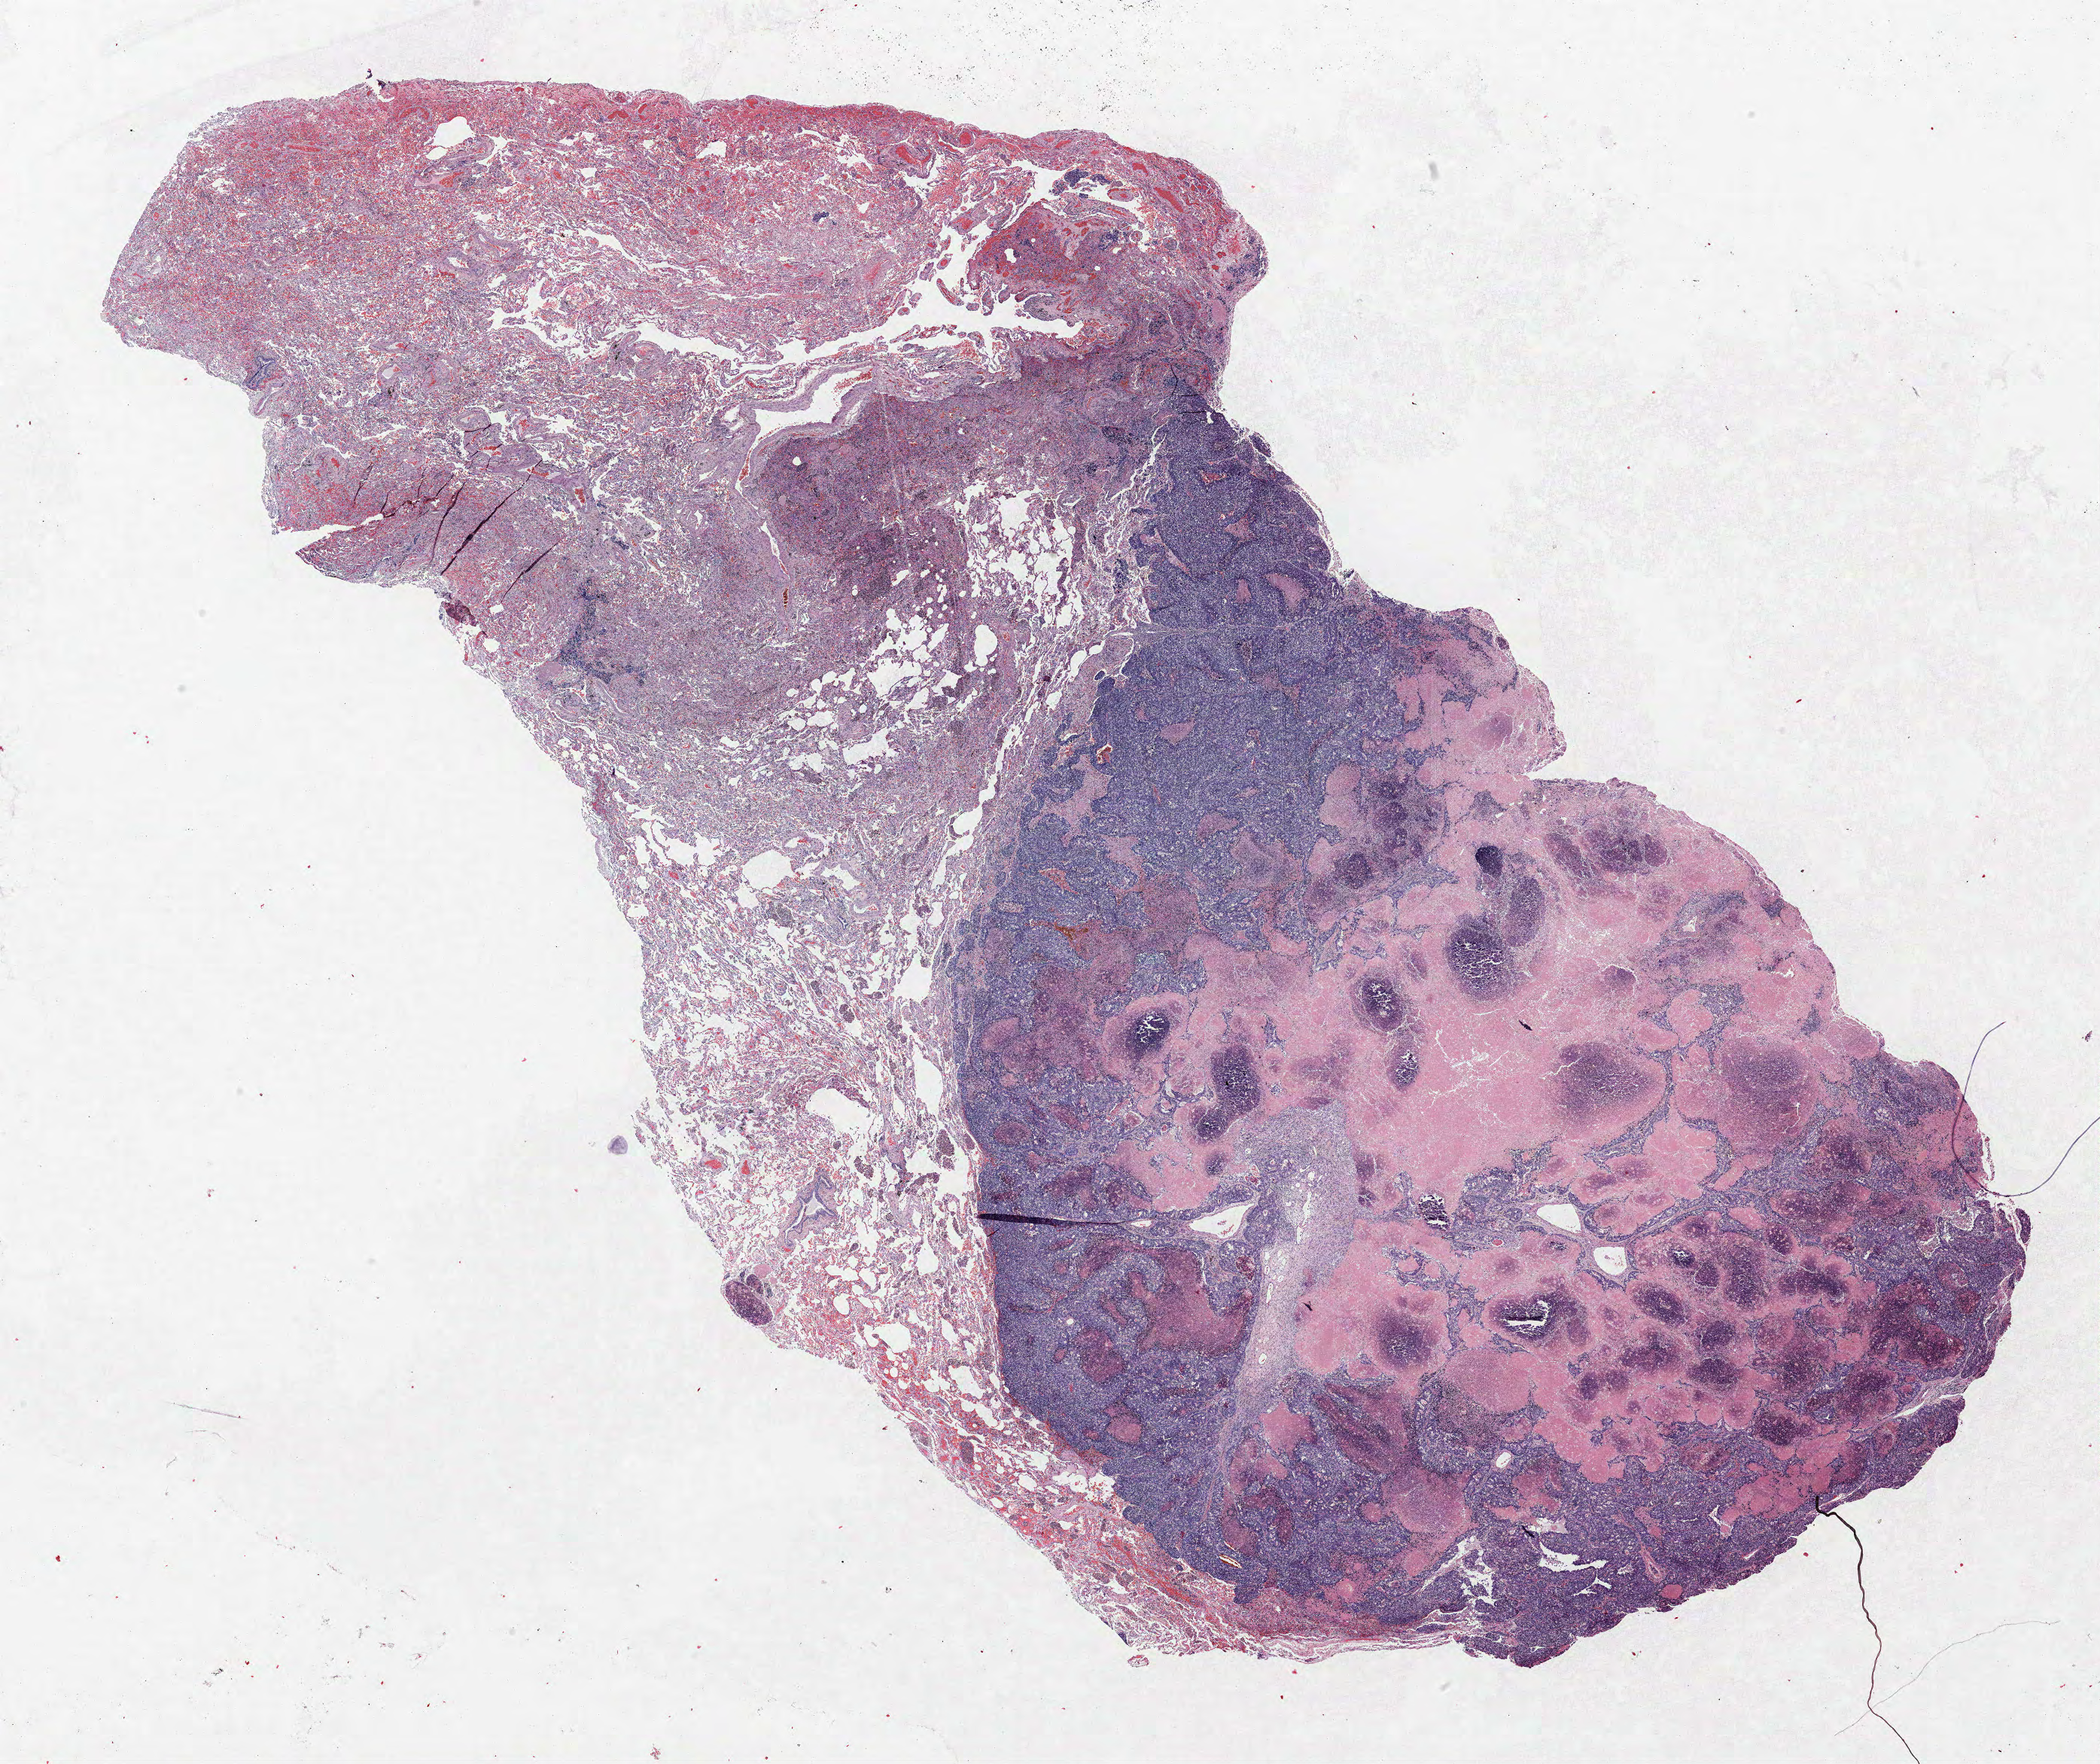
Hematoxylin and eosin (H&E) stained whole-slide image, a low-resolution overview of the entire scanned area, about 22.3 x 18.7 mm, formalin-fixed paraffin-embedded (FFPE) section, lung. Male patient, aged 60 at enrolment.
Participant's lung-cancer diagnosis: Large cell carcinoma, NOS (ICD-O-3 8012/3).